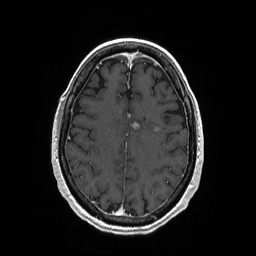
Brain MRI from a brain-tumour surgery series, one axial slice. Slice 73 of 208 in the series (ordered by position). T1-weighted post-contrast. 1 mm slice thickness. 256 × 256 image matrix, field of view 256 × 256 mm. Case-level facts recorded for this patient, not image findings: histopathology: Primary diffuse large B-cell lymphoma; tumour location: Left Corpus Callosum (Frontal).
Outlined on this slice (outlined manually by an expert reader):
- tumour: box from (x=132, y=121) to (x=161, y=132) px